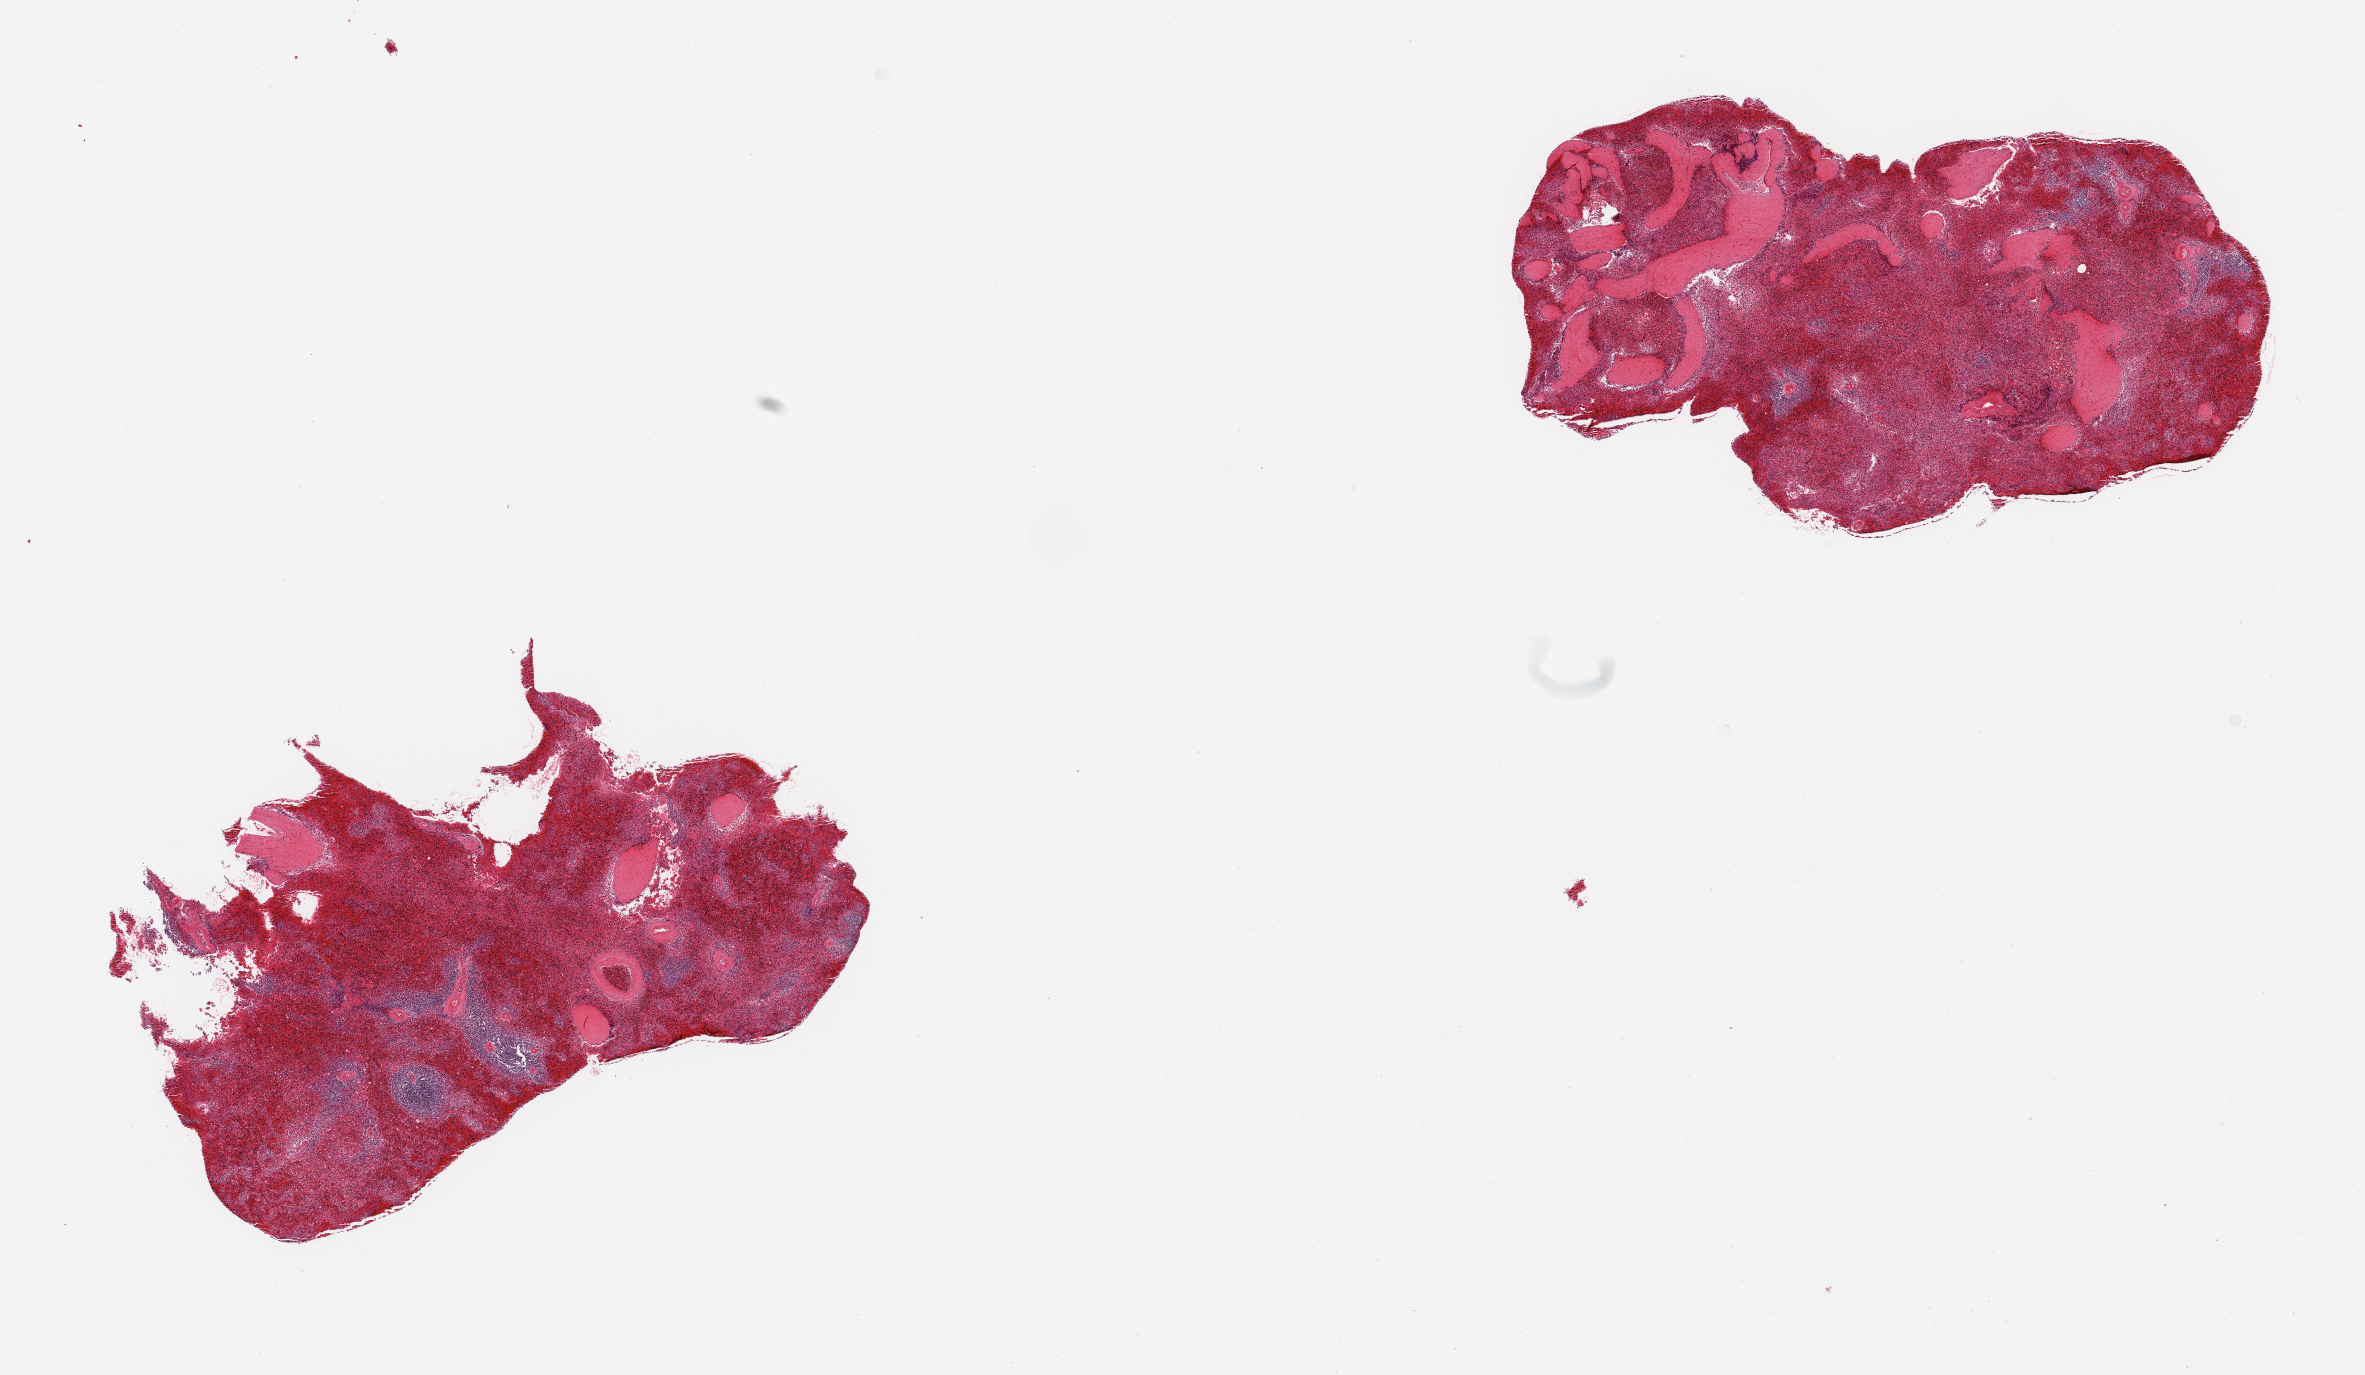
Whole-slide image, H&E stain — low-resolution overview of the scanned area, about 18.7 x 10.9 mm (from a 20x scan); PAXgene-fixed paraffin-embedded (PFPE) section; target tissue: spleen; tissue donor sample. Donor sex: male.
• pathologist's review note for this sample: 2 pieces, Trace macrovesicular steatosis